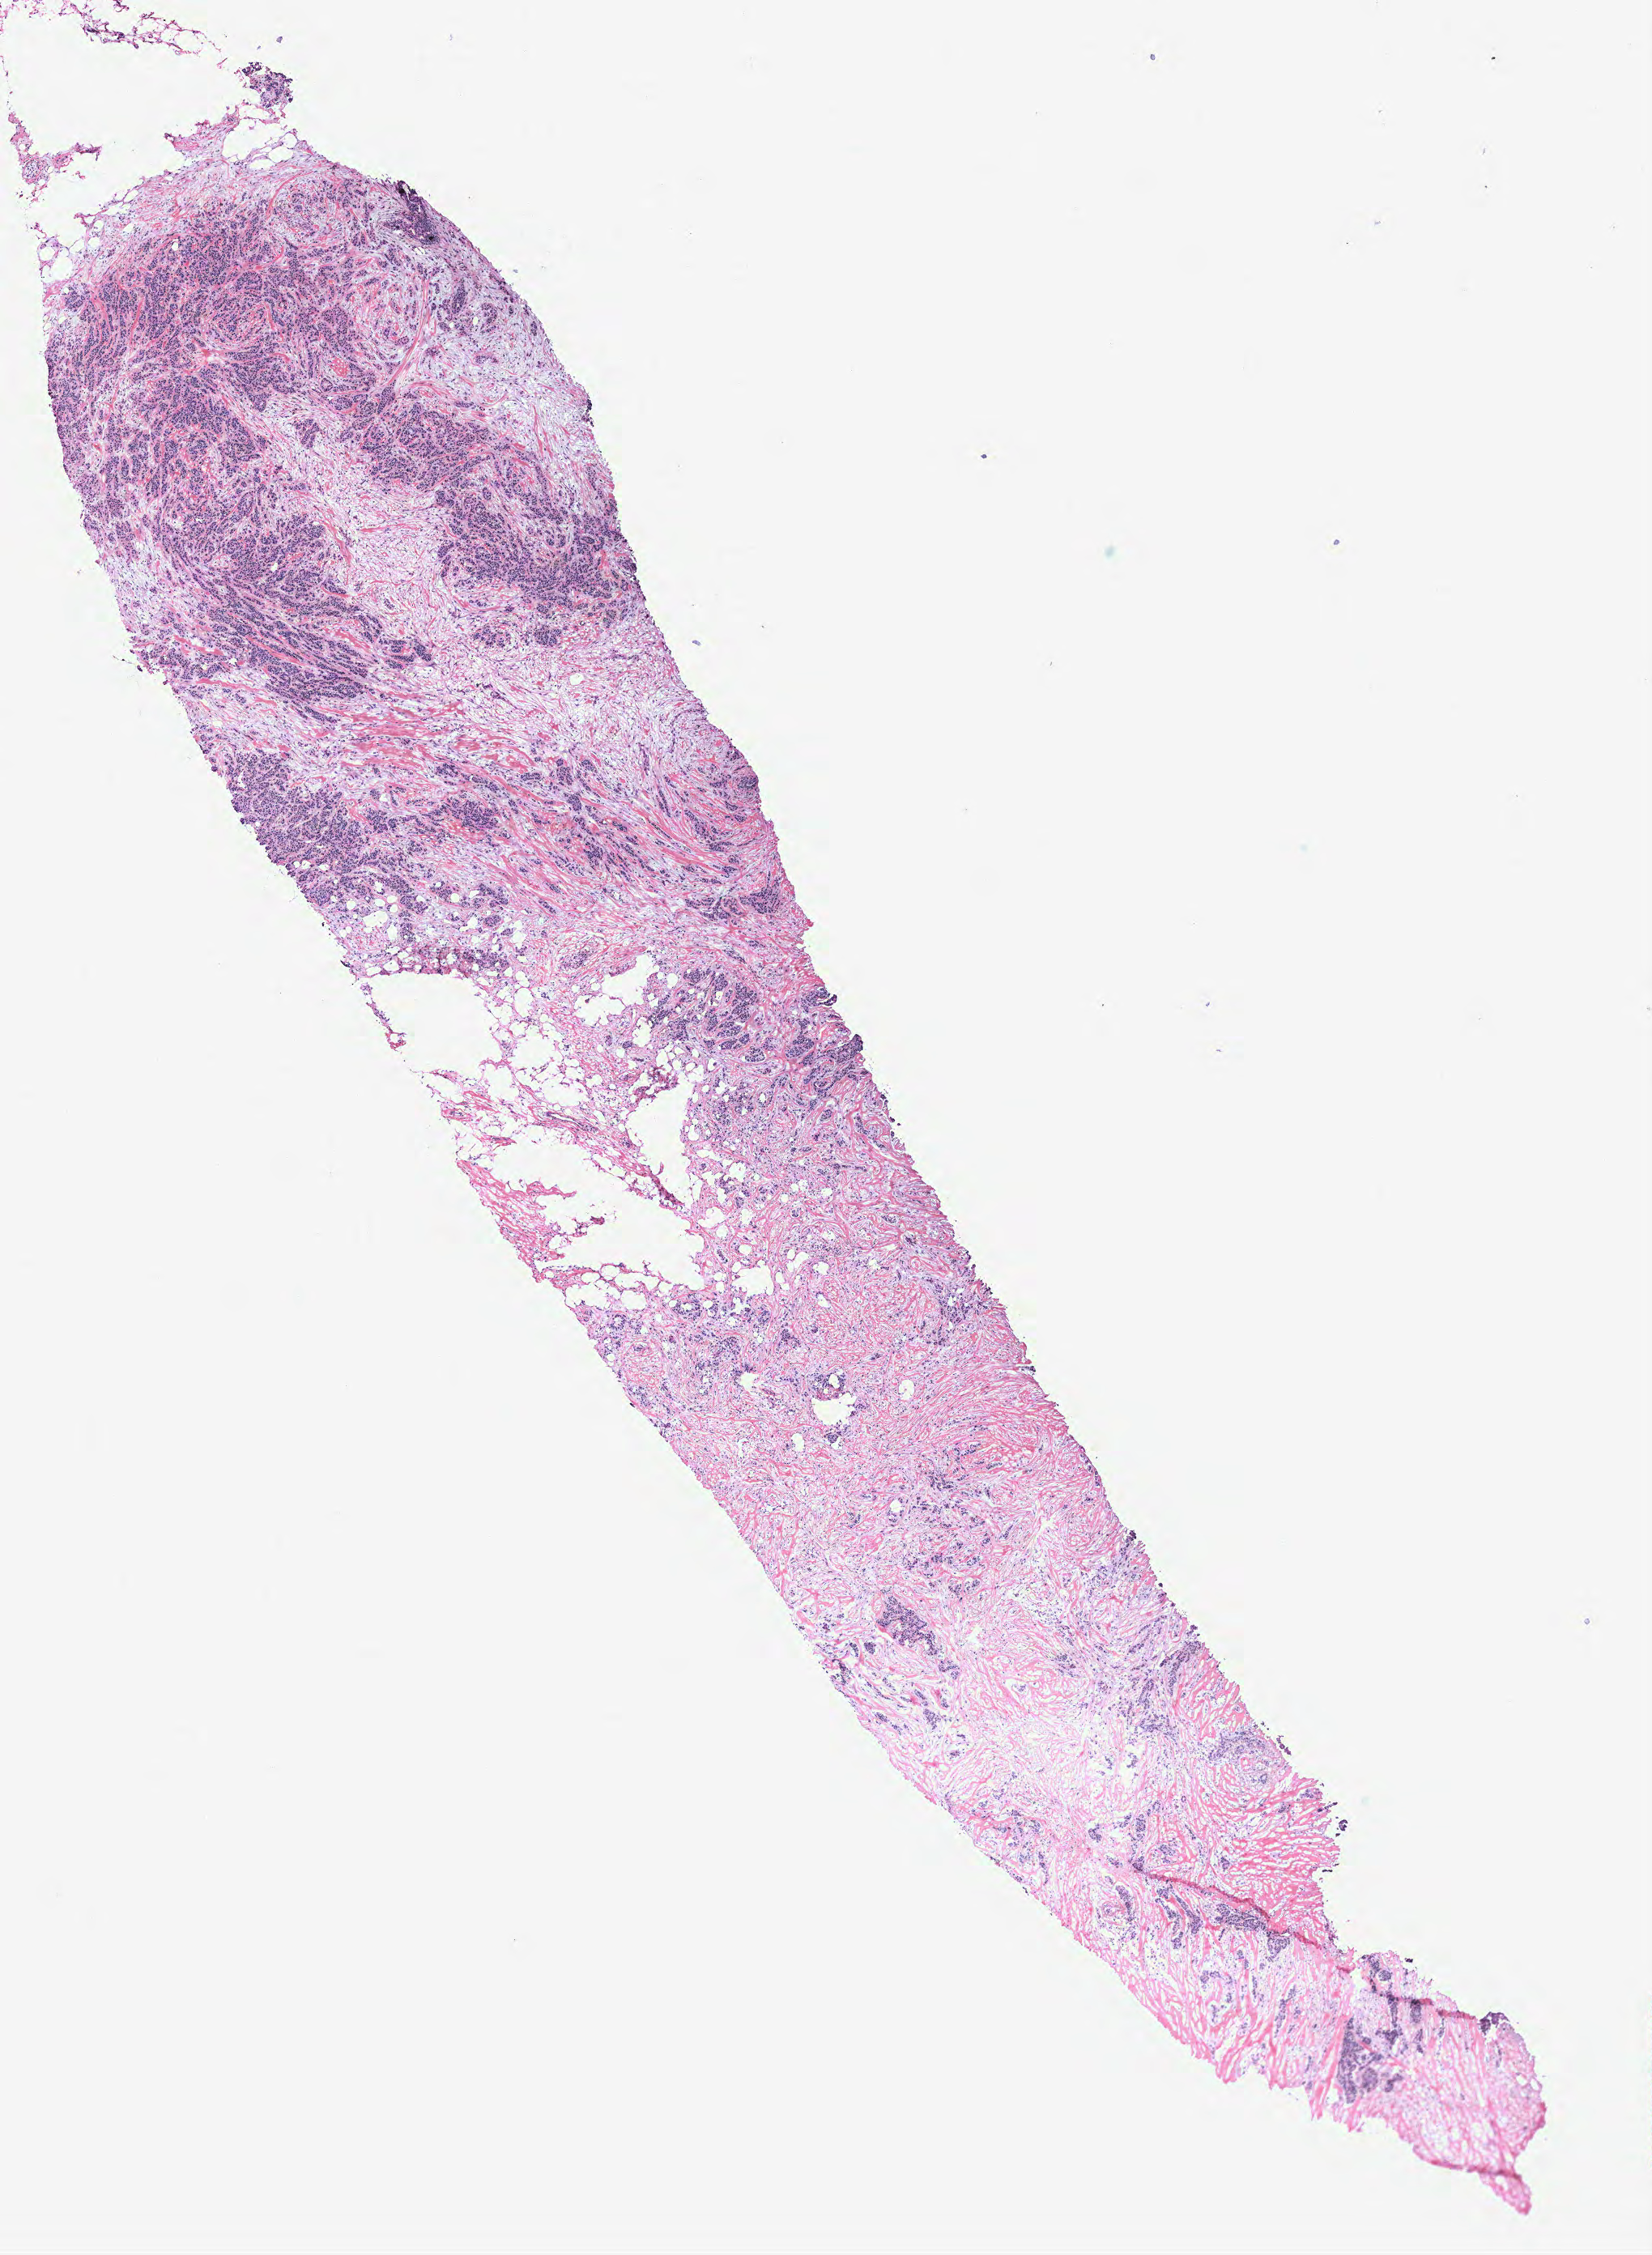
Whole-slide histology image, Hematoxylin and eosin (H&E) stained, low-resolution overview of the scanned area, about 8.2 x 11.1 mm (from a 40x scan). Tumour tissue sample, breast. Female, 52 y/o.
AJCC pathologic stage: IIA. Histologic diagnosis: Infiltrating duct carcinoma, NOS.